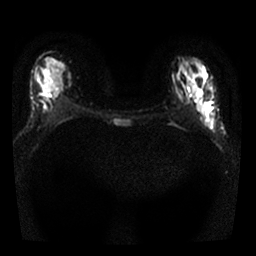
Breast MRI, one axial slice; slice 13 of 25 in the series (ordered by position); diffusion-weighted series; image 2 of 4 stored at this slice position (different b-values; order by instance number); 1.5 T; 4 mm slice thickness; 256 × 256 image matrix, field of view 300 × 300 mm. Female patient.
Annotated regions visible in this slice (expert manual segmentation):
- tumour on diffusion-weighted imaging: bounding box <198,90,215,128> (left, top, right, bottom; pixels)